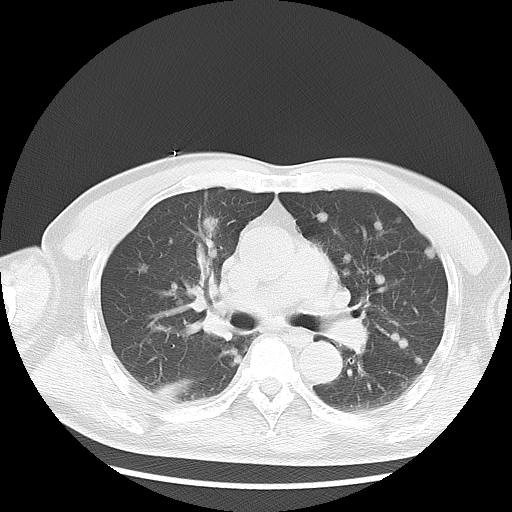
Chest CT, one axial slice. Position 13 of 36 along the scan axis. 120 kVp. Lung window (W 1500 / L -600 HU). 512 × 512 image matrix. Patient: male, 57 years. Case-level facts recorded for this patient, not image findings: clinical TNM (as recorded): T2 N3 M1a.
Annotated regions visible in this slice (bounding box drawn by a radiologist):
- lung tumour (recorded histology: adenocarcinoma): bounding box [x1, y1, x2, y2] px = [195, 214, 220, 235]